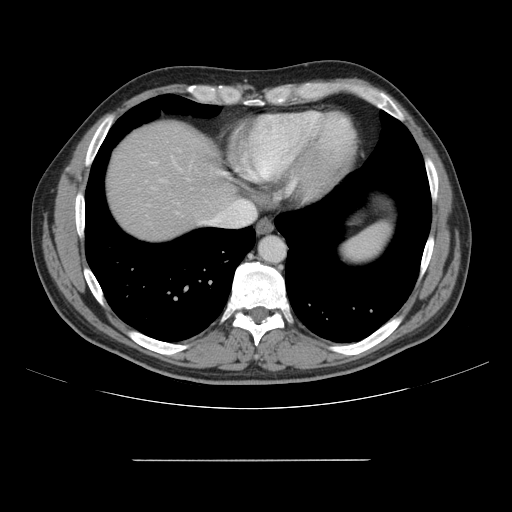
Contrast-enhanced abdominal CT, one axial slice; position 140 of 164 along the scan axis; 120 kVp; intravenous contrast given; soft-tissue window (W 400 / L 40 HU); 512 × 512 image matrix. Male patient, age 54 years. From the clinical record (not read from this slice): diagnosis: colorectal cancer liver metastases, imaged before liver resection; multiple liver metastases: yes; largest metastasis: 1 cm; chemotherapy before resection: yes.
Annotated regions visible in this slice (outlined manually by an expert reader):
- hepatic veins: bounding box <200,200,256,227> (left, top, right, bottom; pixels)
- liver: <106,121,235,241>
- planned liver remnant (the part of the liver to remain after resection): <106,121,234,241>
- portal vein (with intrahepatic branches): <162,163,175,181>